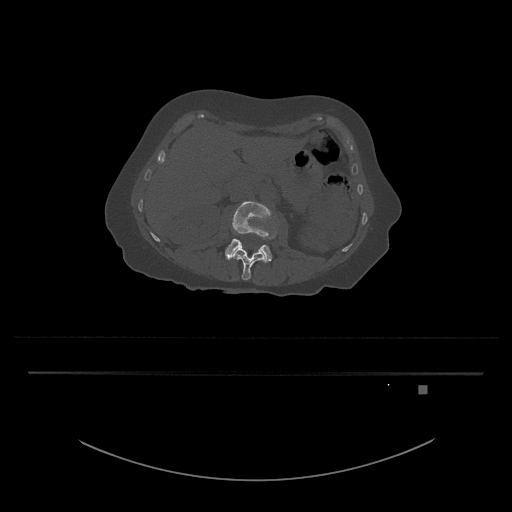
CT including the spine, one axial slice; position 460 of 797 along the scan axis; 120 kVp; bone window (W 1800 / L 400 HU); 512 × 512 image matrix. Female patient, age 57 years. Case-level facts recorded for this patient, not image findings: primary cancer: cervical.
Annotated regions visible in this slice (semi-automatically segmented with operator editing):
- L3 vertebra: bounding box (x1, y1, x2, y2) in pixels: (225, 201, 277, 263)